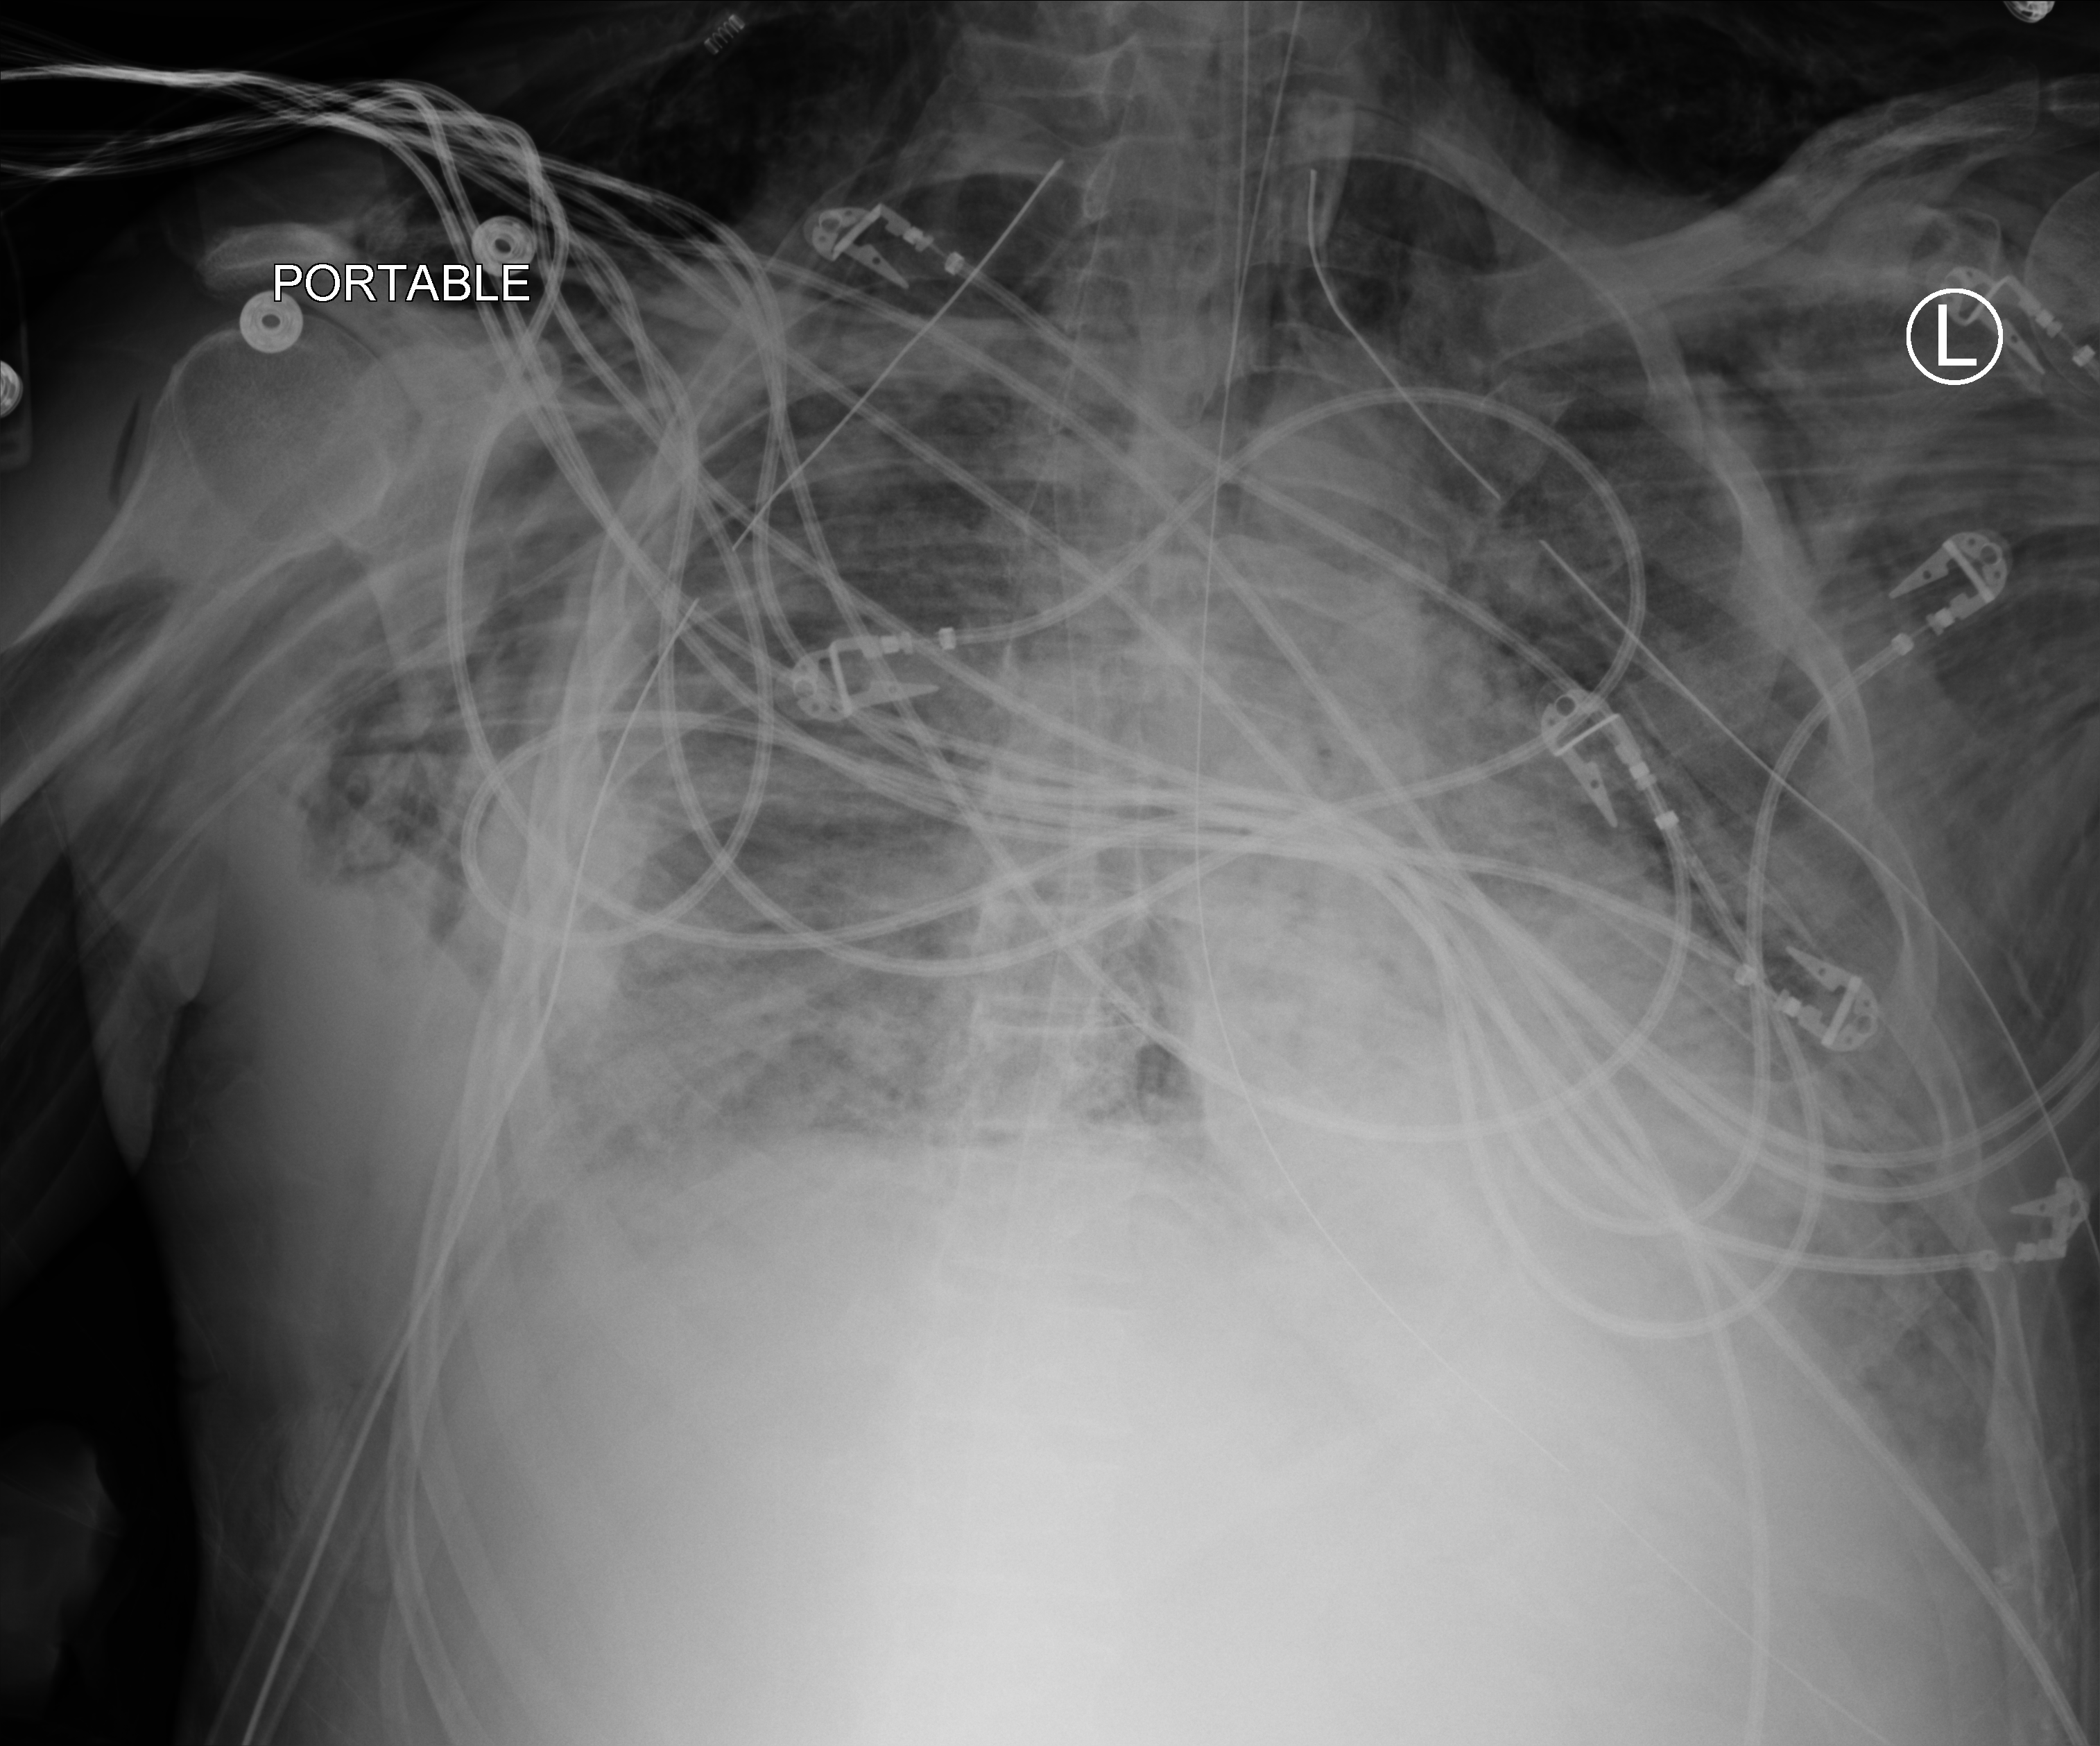
Portable chest radiograph, anteroposterior (AP) projection. Male patient hospitalised with COVID-19, age 18–59 years.
From the hospital-stay record, not from the radiograph (when in the stay this image was taken is not recorded): mechanically ventilated during this hospital stay: yes; other chronic lung disease (admission record): no.